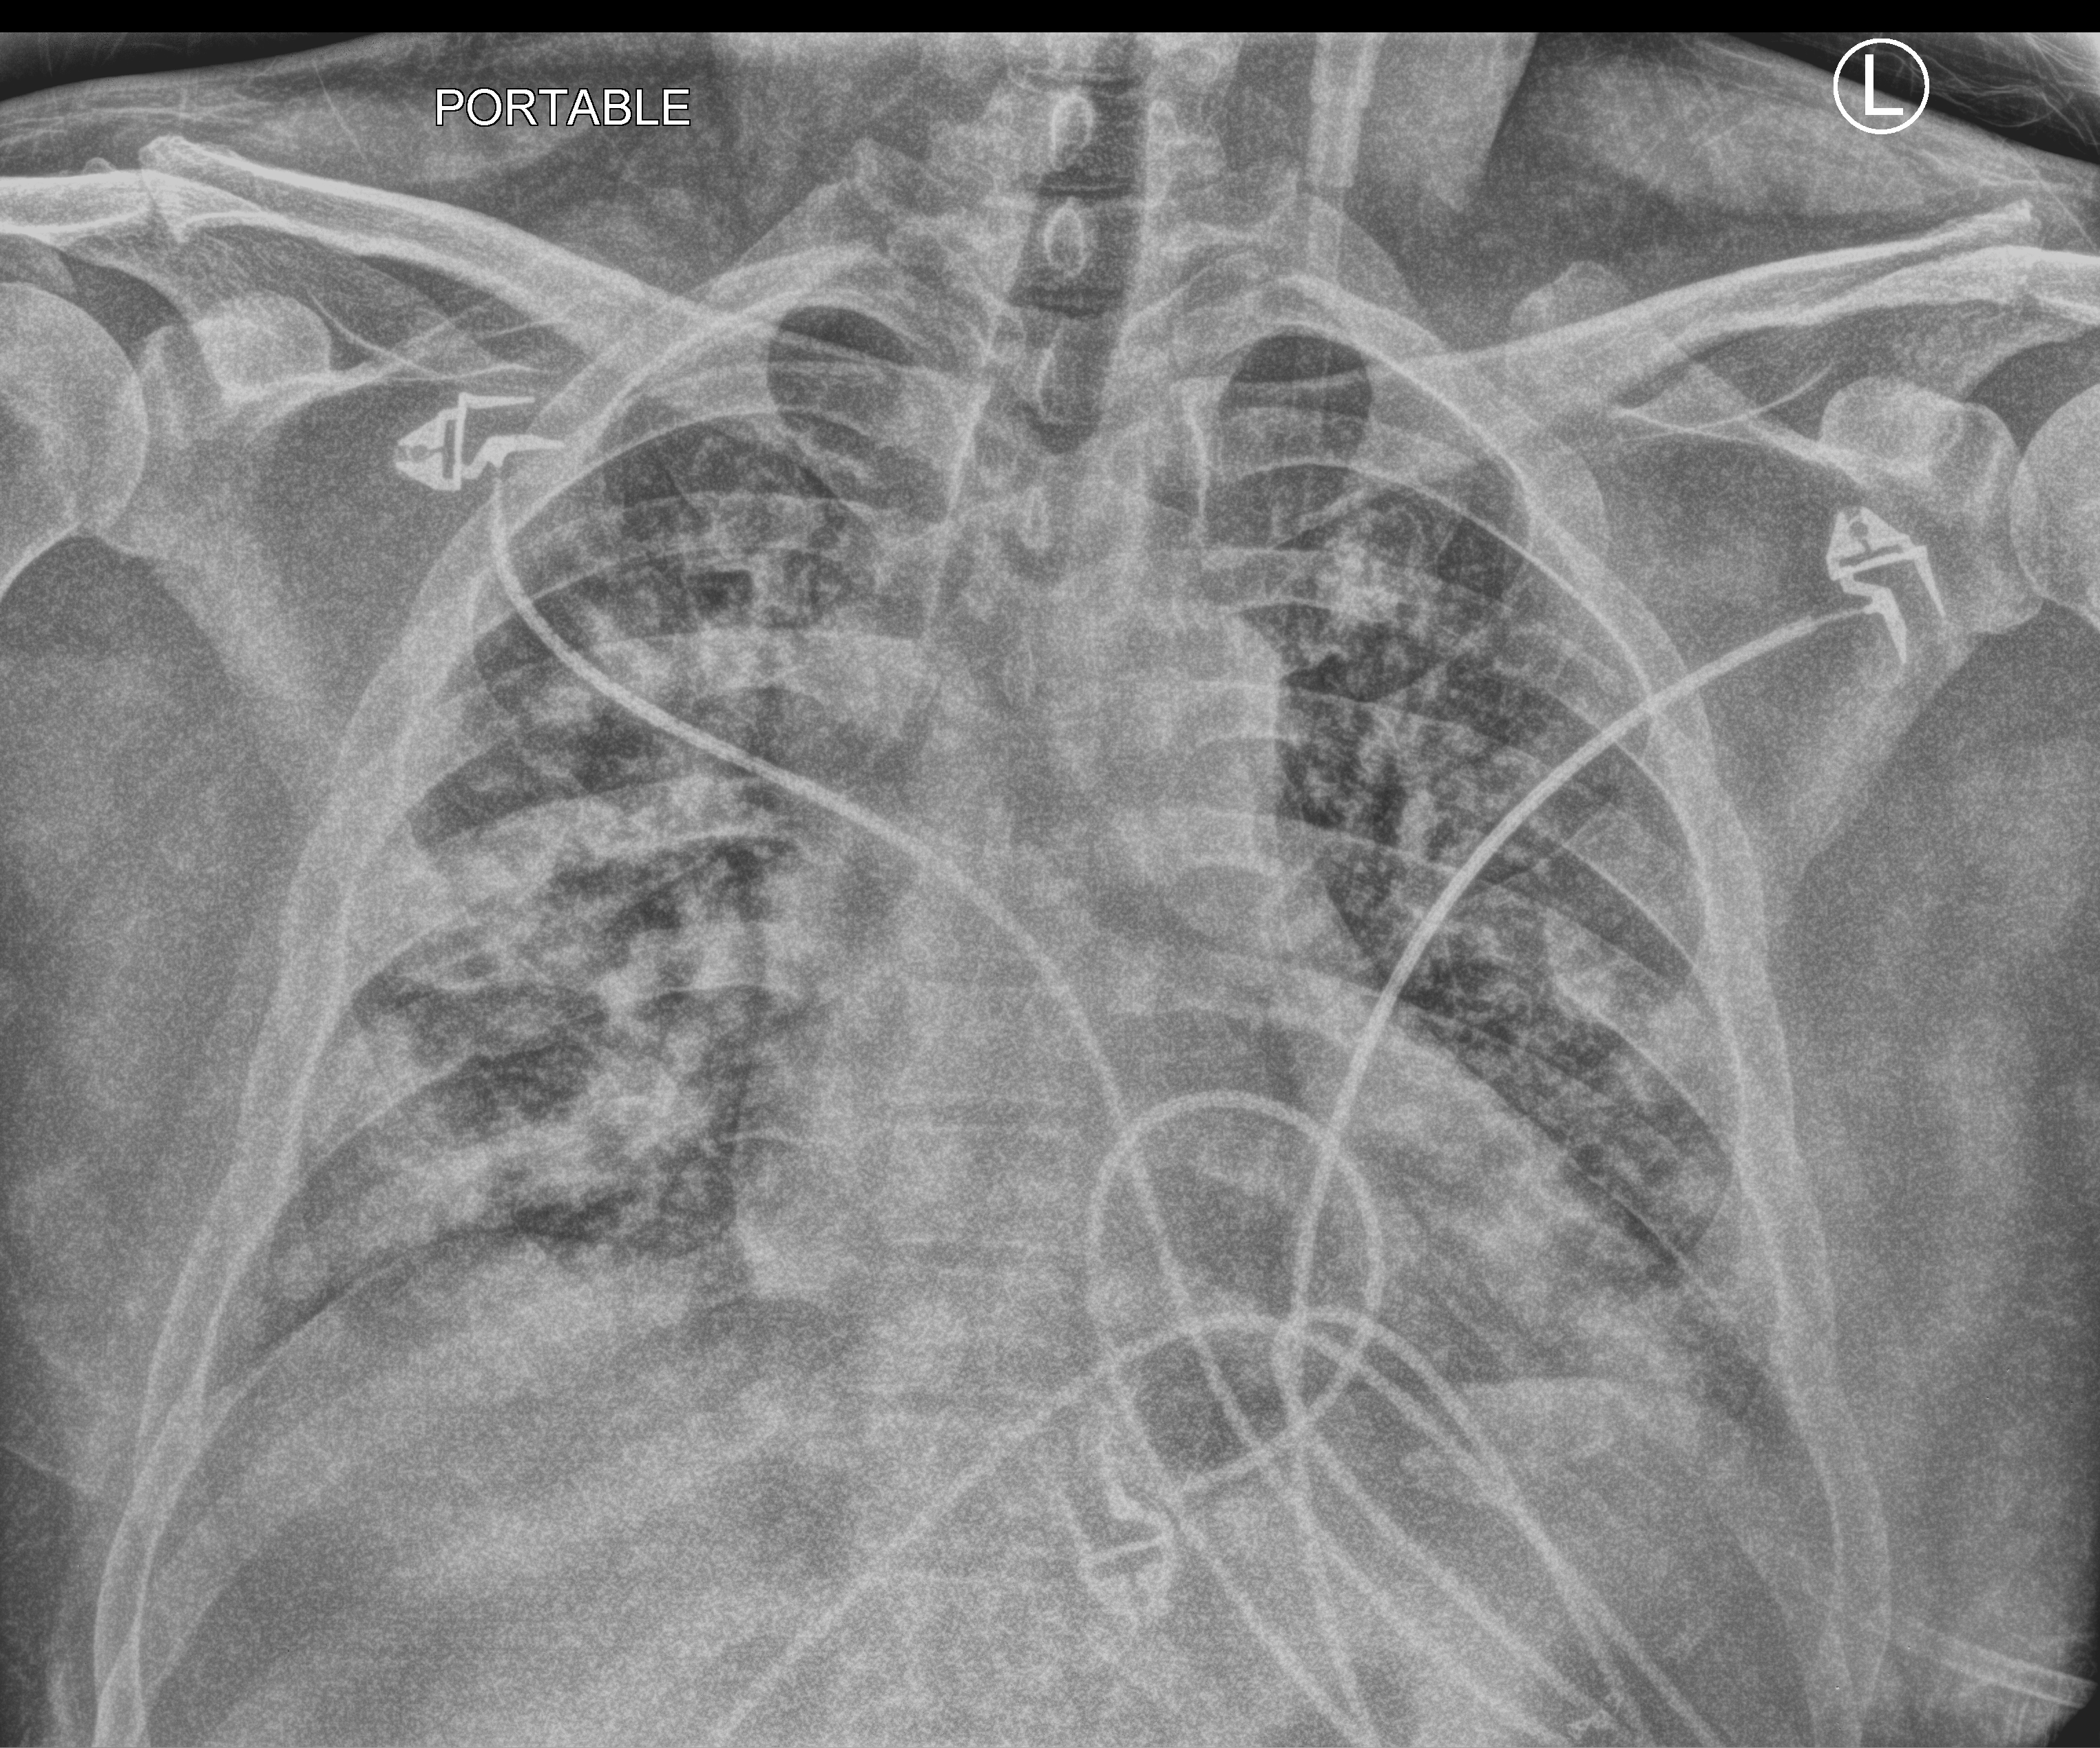
Chest X-ray (portable); anteroposterior (AP) projection. Male patient hospitalised with COVID-19, age 18–59 years.
From the hospital-stay record, not from the radiograph (when in the stay this image was taken is not recorded): length of hospital stay: 8 days.